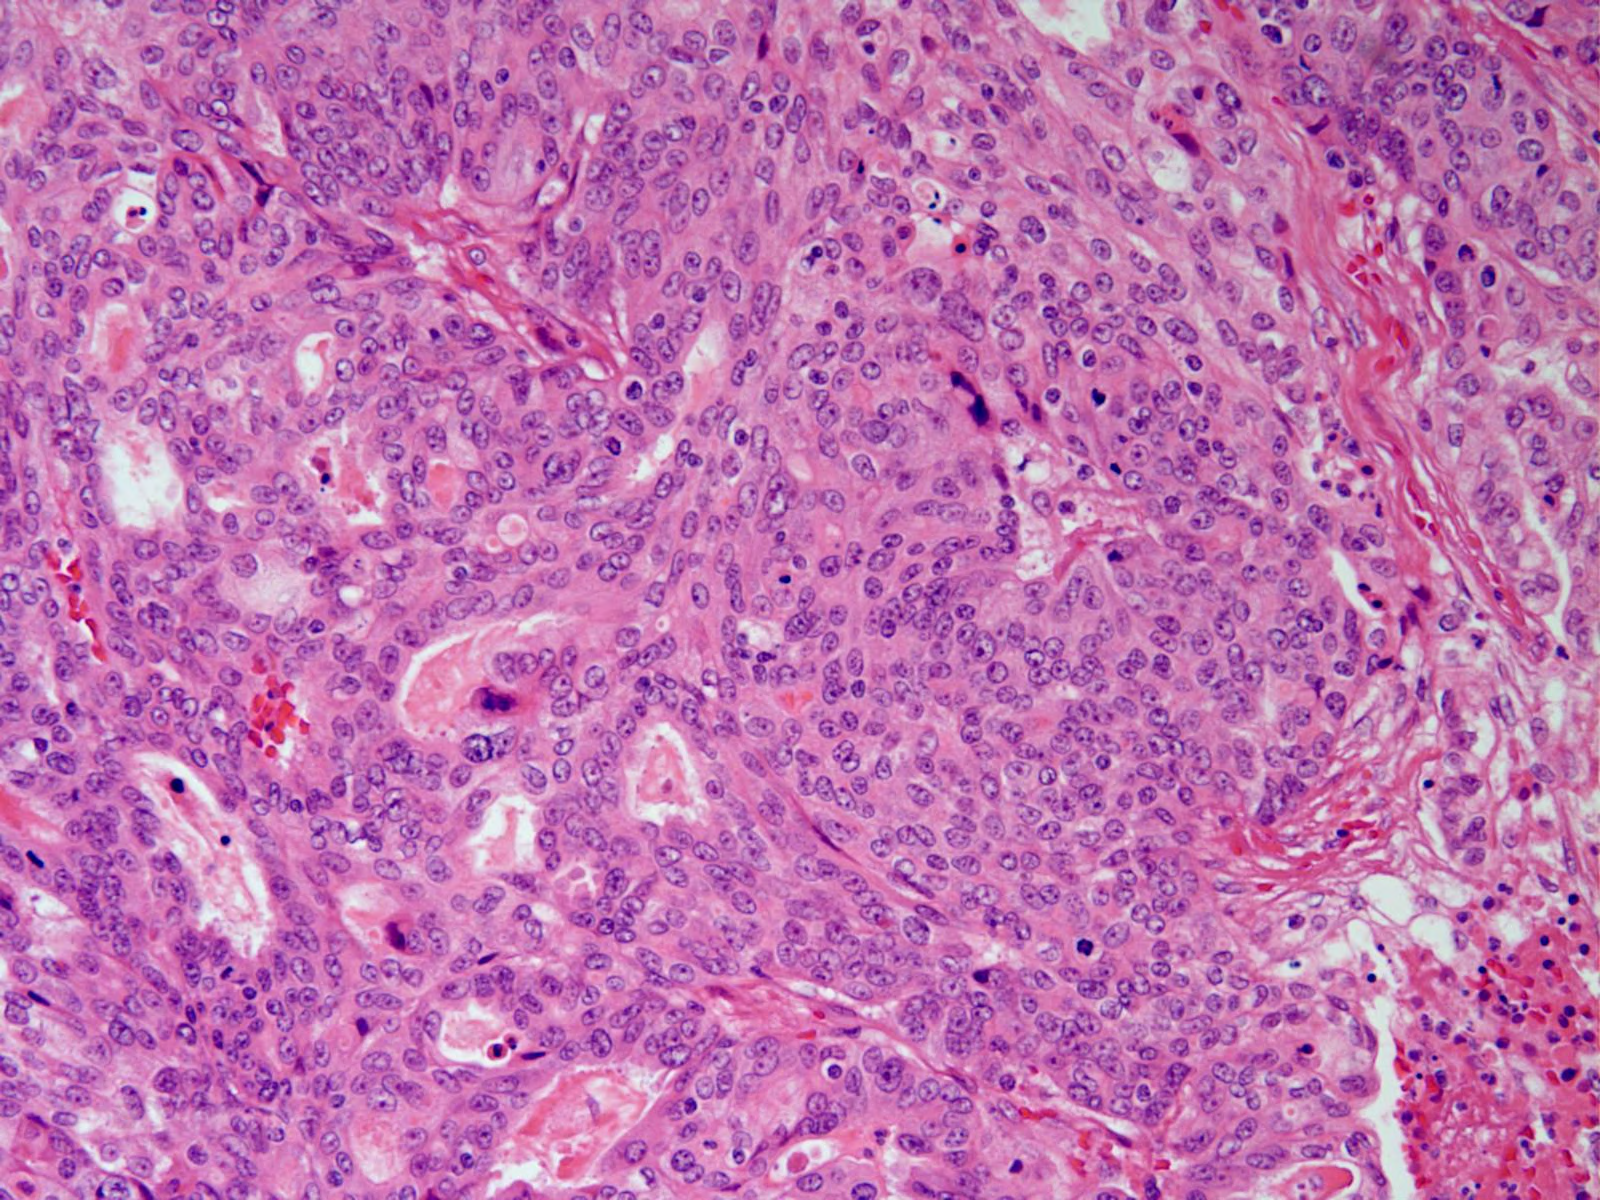
Single-field H&E photomicrograph — roughly 0.8 x 0.6 mm in extent. FFPE section. Sample: primary tumour, stomach. Patient: male, age at initial diagnosis 80 years. Histologic grade: G2 (moderately differentiated).
Lymph nodes positive (case pathology): 3 of 8 examined. Diagnosis: Adenocarcinoma, NOS (gastric antrum).